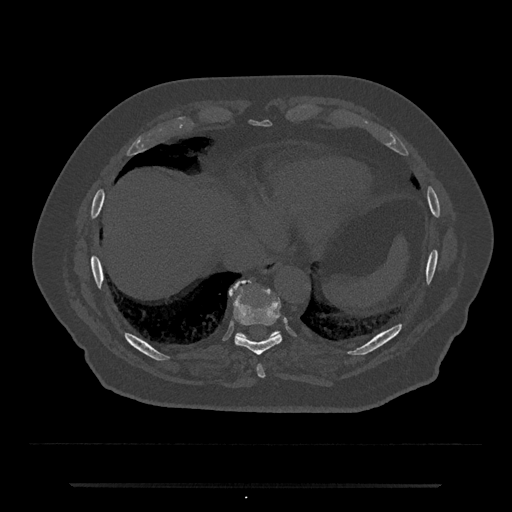
CT including the spine, one axial slice; position 747 of 797 along the scan axis; bone window (W 1800 / L 400 HU); 512 × 512 image matrix, field of view 434 × 434 mm. Male patient, age 80 years. Case-level facts recorded for this patient, not image findings: primary cancer: prostate.
Annotated regions visible in this slice (semi-automatically segmented with operator editing):
- T10 vertebra: bounding box [x1, y1, x2, y2] px = [230, 282, 281, 339]
- T8 vertebra: [257, 364, 265, 378]
- T9 vertebra: [234, 301, 282, 356]